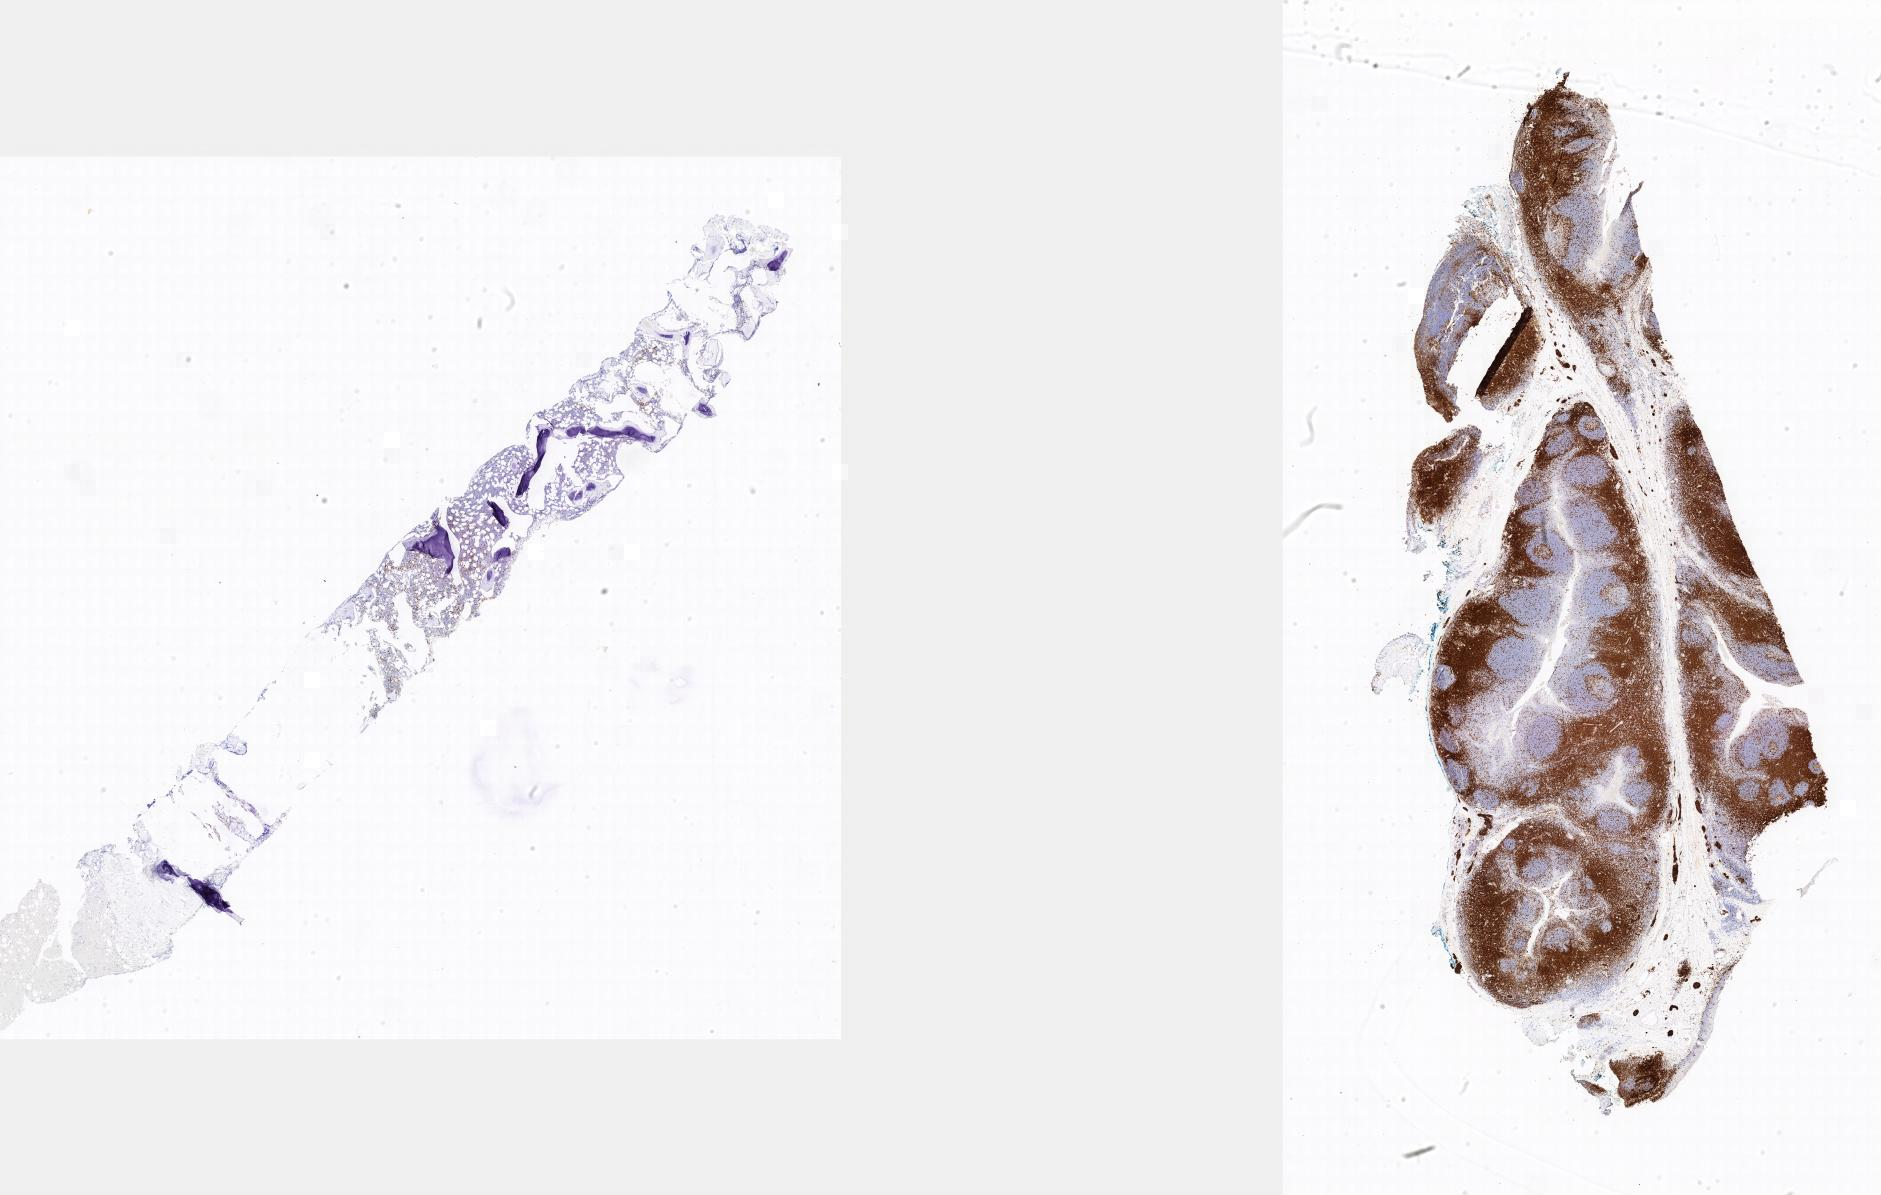
IHC for CD3, whole-slide image — whole scanned area shown as a low-resolution overview; specimen: tumor tissue; site: bone marrow. Patient male; aged 15.
- diagnosis: Burkitt lymphoma, NOS